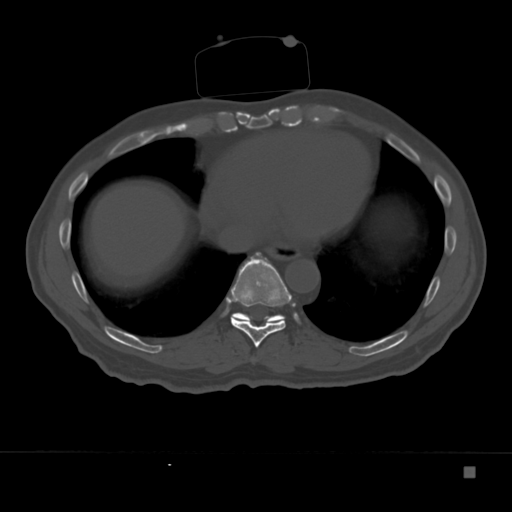
CT including the spine, one axial slice; slice 185 of 332 in the series (ordered by position); 120 kVp; bone window (W 1800 / L 400 HU); 1.5 mm slice thickness; 512 × 512 image matrix, field of view 389 × 389 mm. Patient: male, 72 years. Case-level facts recorded for this patient, not image findings: primary cancer: skeletal.
Structures marked on this image (semi-automatically segmented with operator editing):
- T10 vertebra: bounding box <231,313,281,320> (left, top, right, bottom; pixels)
- T9 vertebra: <230,252,292,348>